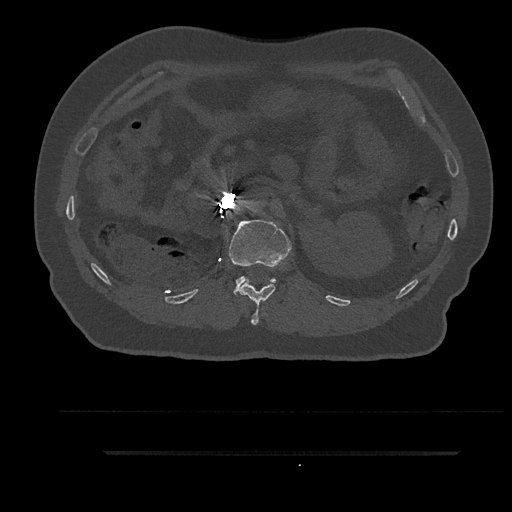
CT including the spine, one axial slice. Position 205 of 797 along the scan axis. Bone window (W 1800 / L 400 HU). 0.5 mm slice thickness. 512 × 512 image matrix. Patient: male, 63 years. Case-level facts recorded for this patient, not image findings: primary cancer: renal; vertebrae with lytic lesions (as recorded): T8.
Annotated regions visible in this slice (semi-automatically segmented with operator editing):
- L1 vertebra: bounding box (x1, y1, x2, y2) in pixels: (228, 219, 292, 295)
- T12 vertebra: (239, 281, 275, 325)